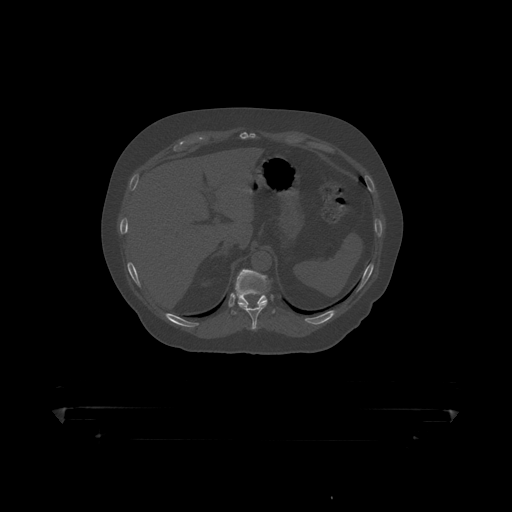
CT including the spine, one axial slice. Slice 206 of 390 in the series (ordered by position). Reconstruction kernel STANDARD. 120 kVp. Bone window (W 1800 / L 400 HU). 1.25 mm slice thickness. 512 × 512 image matrix, field of view 650 × 650 mm. Patient: male, 60 years. Case-level facts recorded for this patient, not image findings: primary cancer: prostate.
Outlined on this slice (semi-automatically segmented with operator editing):
- T10 vertebra: bounding box [x1, y1, x2, y2] px = [239, 301, 268, 319]
- T11 vertebra: [230, 270, 276, 315]